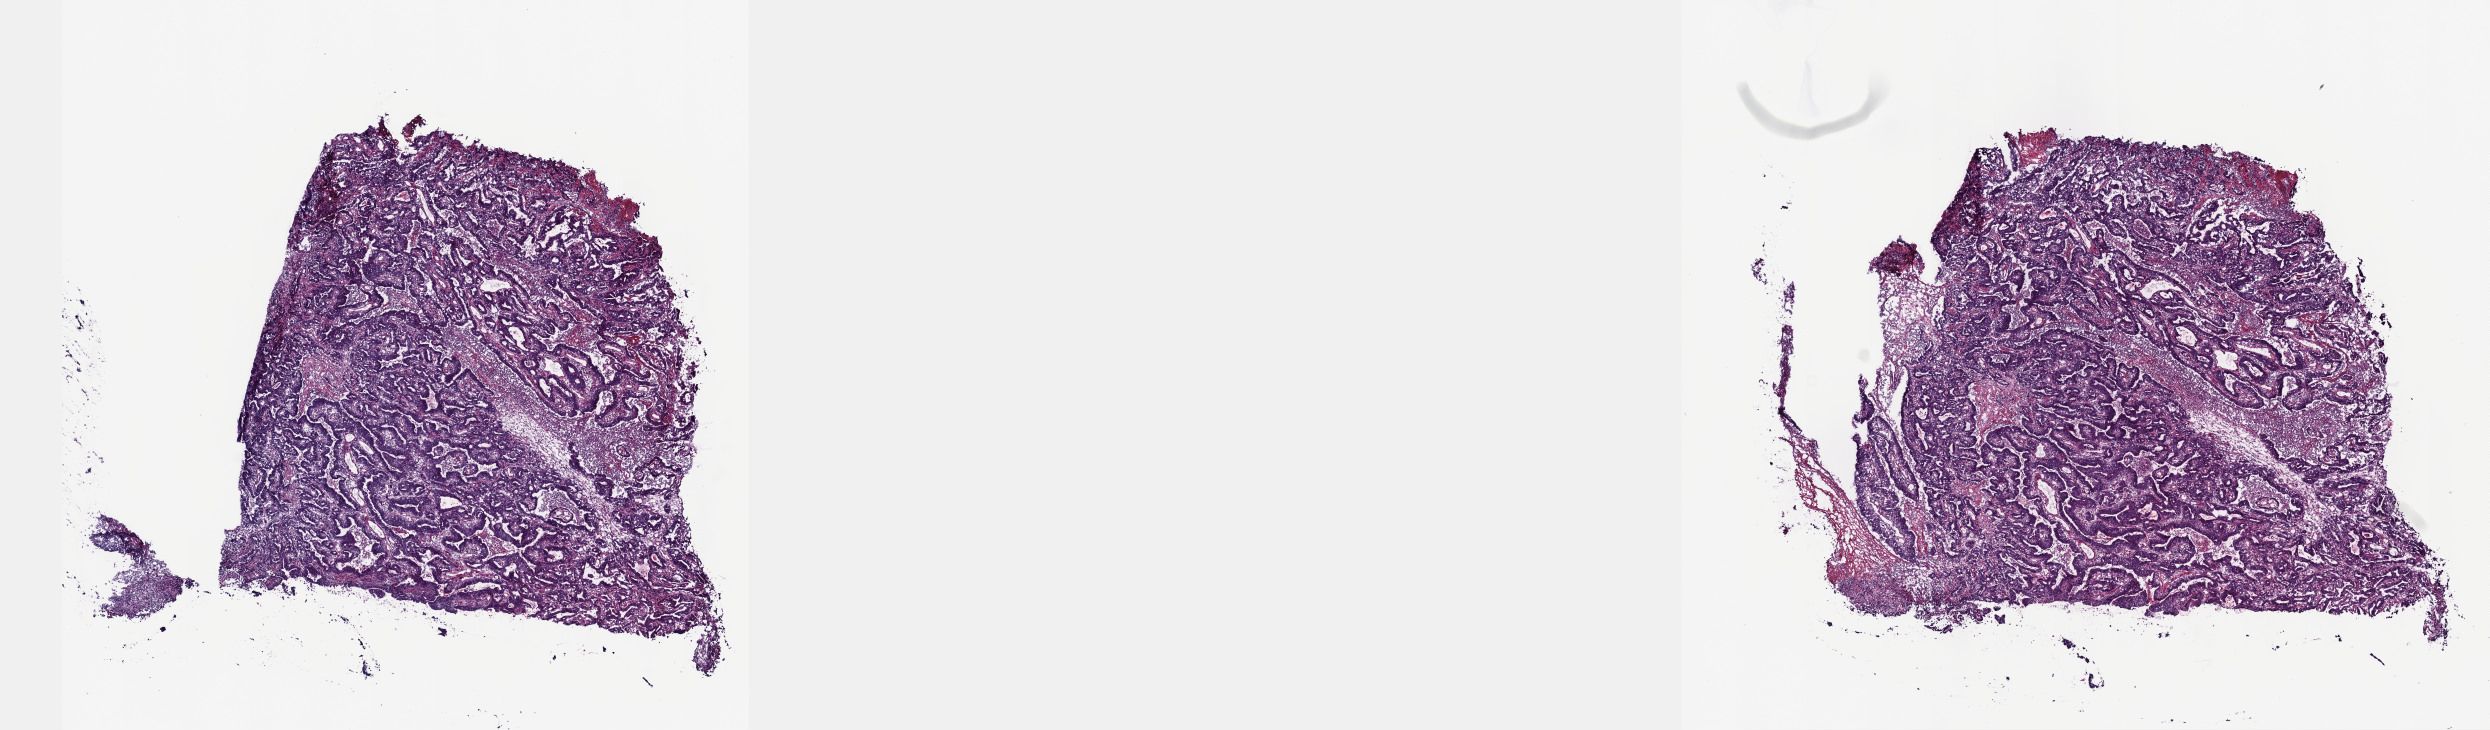
Digitized H&E-stained tissue section (whole slide) — low-resolution overview of the scanned area, about 20.1 x 5.9 mm (from a 40x scan), frozen section from the top of the tissue portion, esophagus, primary tumour sample. Male patient; age at initial diagnosis 73 years. Histologic grade: G2 (moderately differentiated). Pathologist review of this section (percent, as recorded): tumour cells 57%, tumour nuclei 65%, normal cells 0%, stromal cells 40%, necrosis 3%. Inflammatory infiltration, as recorded: lymphocyte infiltration 15%, monocyte infiltration 3%, neutrophil infiltration 15%.
TNM: T3 N1 M0. Pathologic diagnosis: Tubular adenocarcinoma. AJCC pathologic stage: III (6th edition).